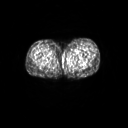
FDG PET of an extremity soft-tissue mass (from a PET/CT study), one axial slice. Position 31 of 267 along the scan axis. 3.27 mm slice thickness. 128 × 128 image matrix, field of view 600 × 600 mm. Female patient, age 24 years. From the clinical record (not read from this slice): histological type: leiomyosarcoma; grade: high; site of the primary tumour: groin.
Structures marked on this image (expert contour drawn on MRI and transferred to this co-registered scan by the dataset authors):
- gross tumour volume including surrounding oedema: bounding box (x1, y1, x2, y2) in pixels: (63, 61, 64, 62)